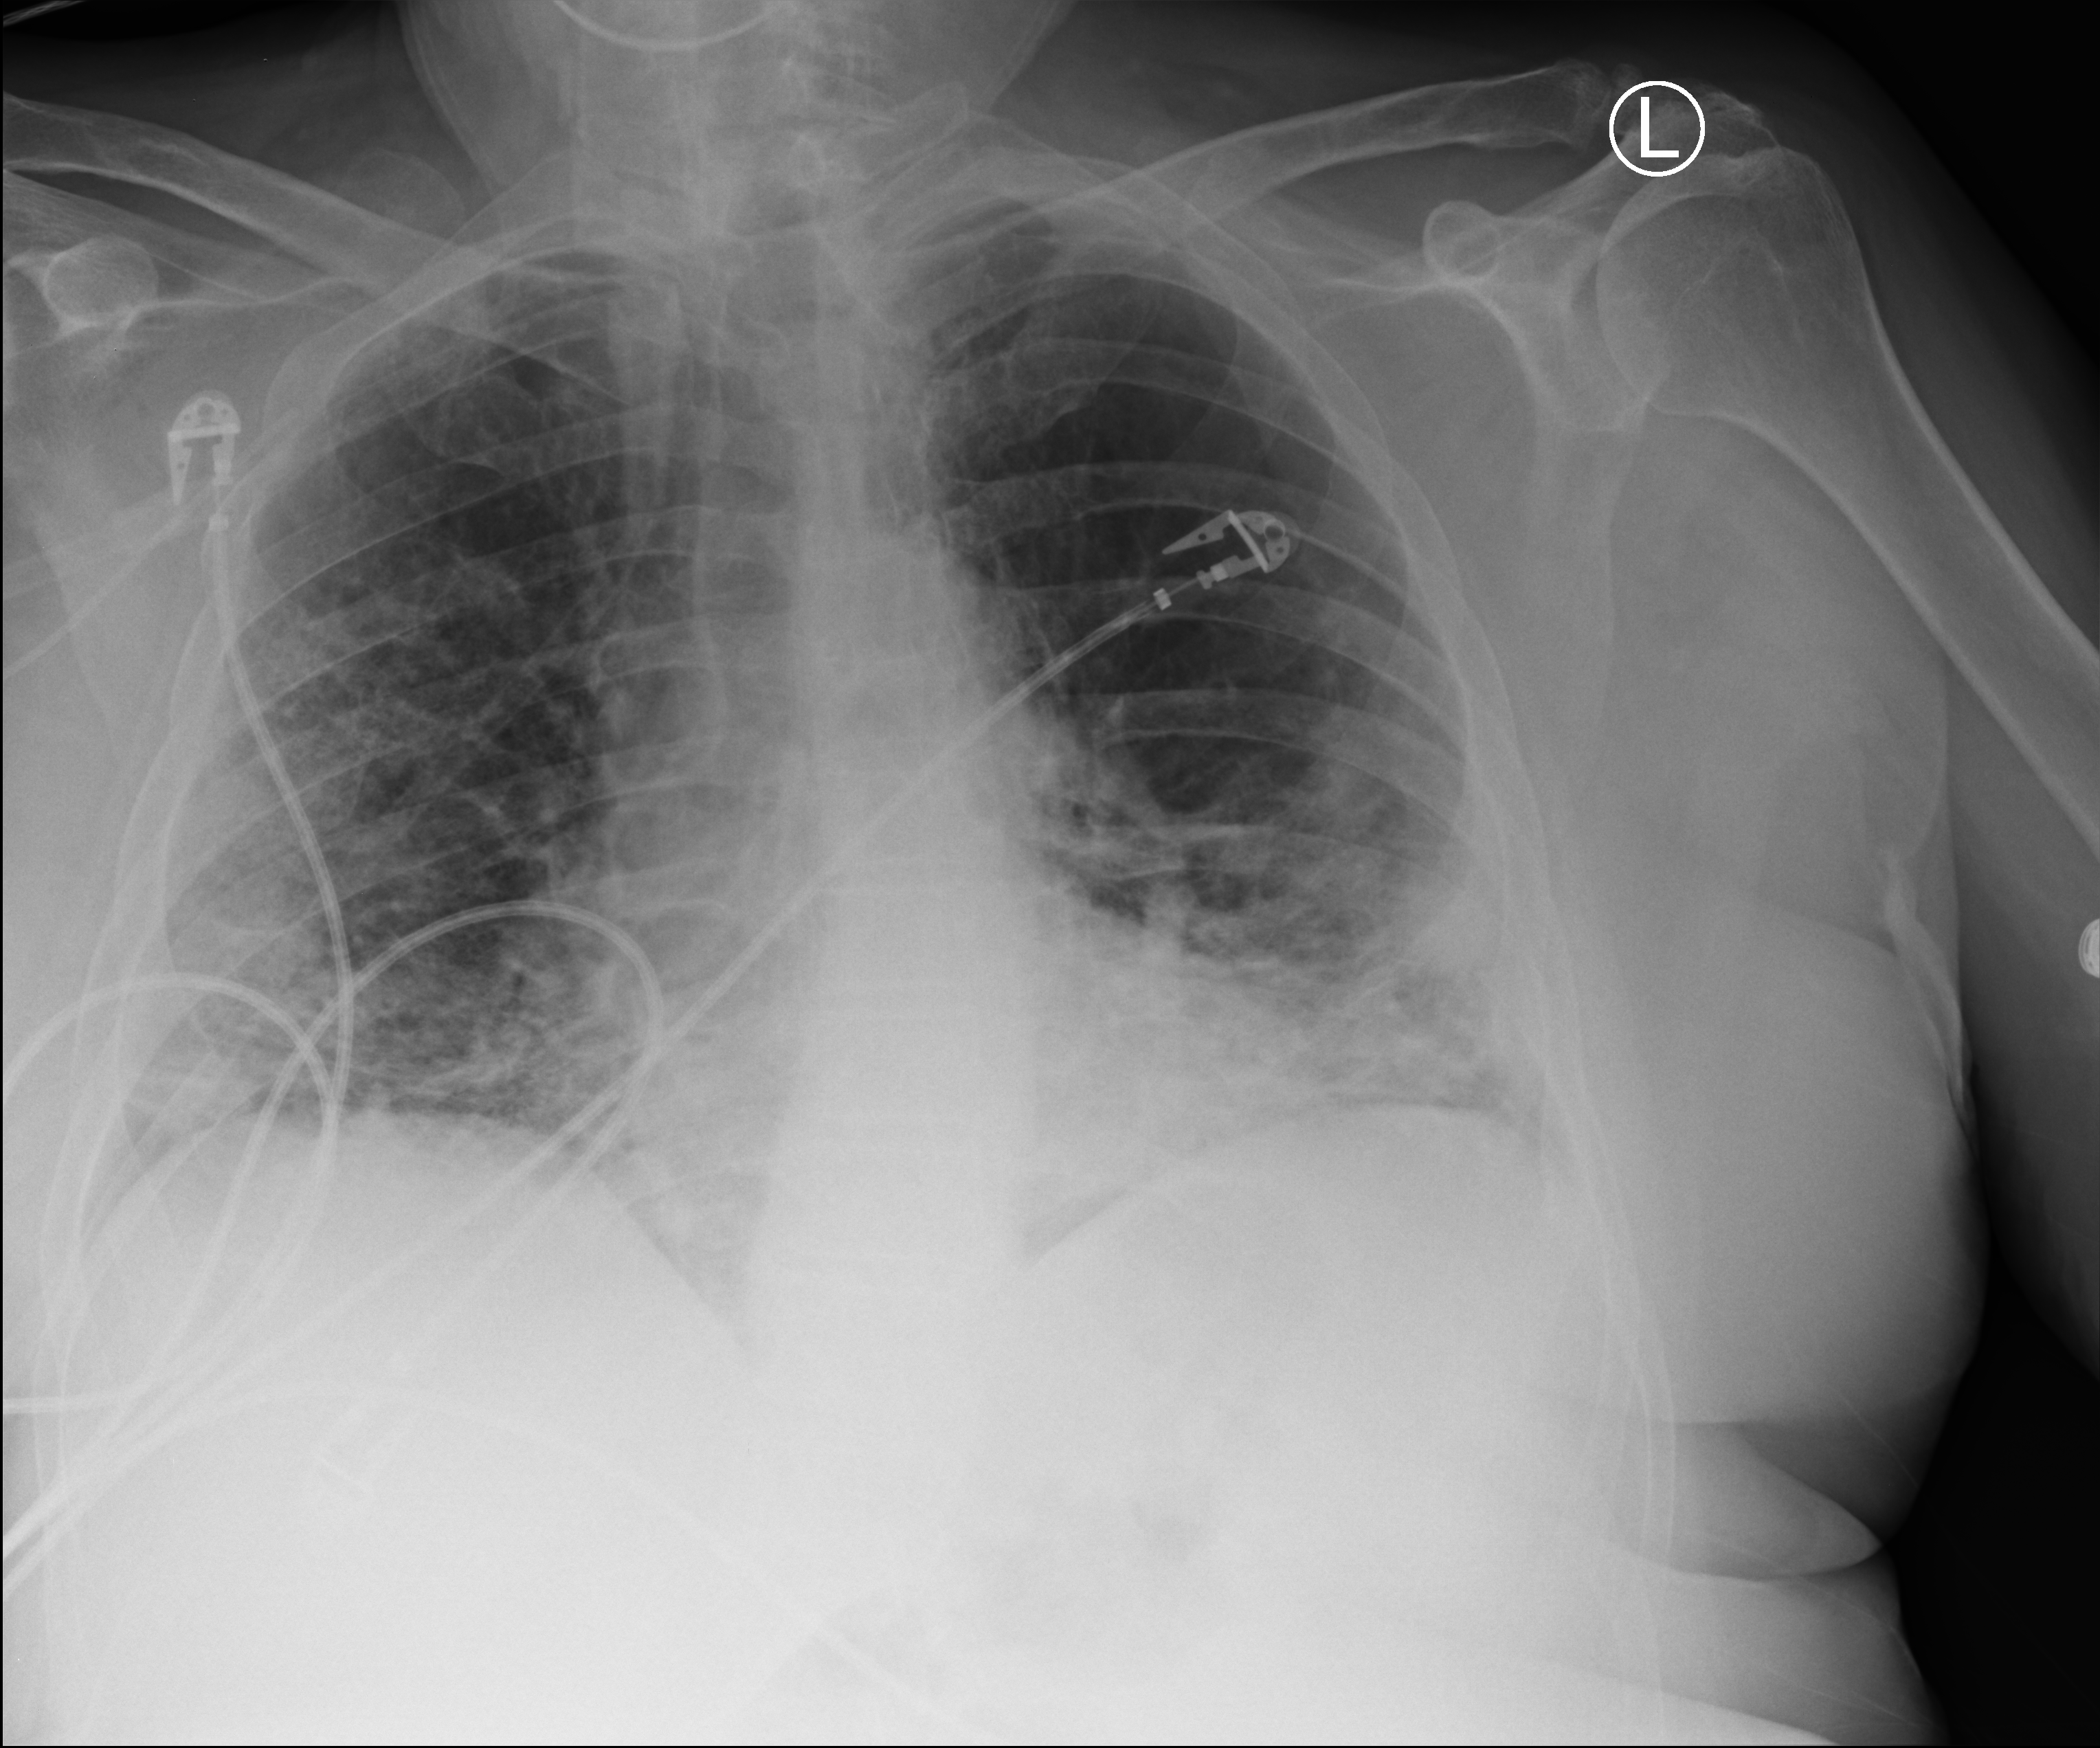
Portable chest radiograph, anteroposterior (AP) projection. Patient hospitalised with COVID-19; male, aged 60–74 years.
Admission-level facts for this patient (not findings on this image; timing relative to this image not recorded): admitted to intensive care during this hospital stay: no; hypertension (admission record): no; mechanically ventilated during this hospital stay: no.